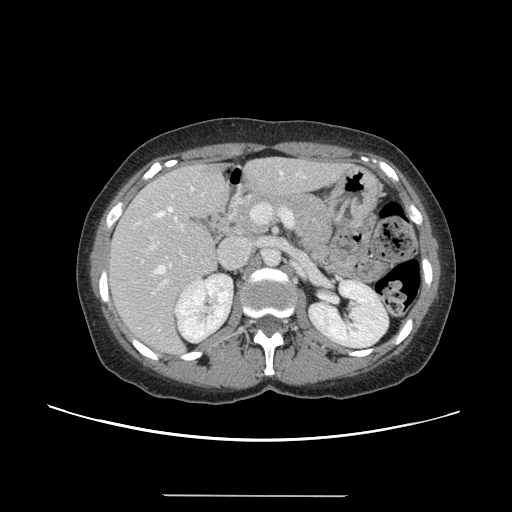
Contrast-enhanced abdominal CT, one axial slice; slice 75 of 144 in the series (ordered by position); intravenous contrast given; soft-tissue window (W 400 / L 40 HU); 2.5 mm slice thickness; 512 × 512 image matrix, field of view 380 × 380 mm. Female patient, age 53 years. Case-level facts recorded for this patient, not image findings: diagnosis: colorectal cancer liver metastases, imaged before liver resection; multiple liver metastases: yes; largest metastasis: 1.1 cm; disease in both lobes: no.
Annotated regions visible in this slice (manually delineated by an expert):
- hepatic veins: bounding box [x1, y1, x2, y2] px = [154, 171, 283, 273]
- liver: [109, 159, 342, 354]
- planned liver remnant (the part of the liver to remain after resection): [110, 159, 319, 300]
- portal vein (with intrahepatic branches): [142, 204, 294, 294]